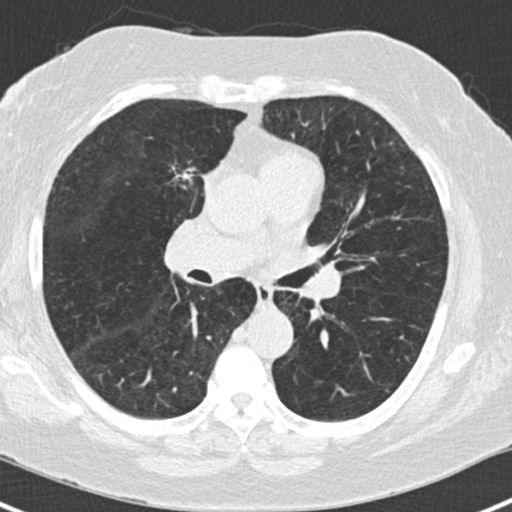
Low-dose screening chest CT, one axial slice. Slice 85 of 168 in the series (ordered by position). 120 kVp. Lung window (W 1500 / L -600 HU). 2 mm slice thickness. 512 × 512 image matrix, field of view 303 × 303 mm.
Annotated regions visible in this slice (outlined manually by an expert reader):
- lesion 1 (tumor, upper lobe of right lung): bounding box (x1, y1, x2, y2) in pixels: (171, 167, 196, 190)